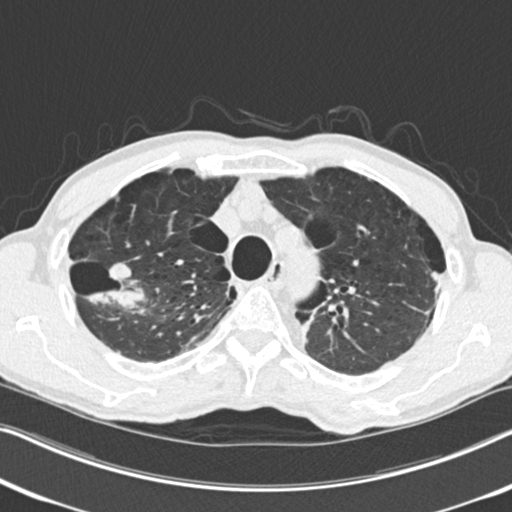
Low-dose screening chest CT, one axial slice; slice 195 of 251 in the series (ordered by position); reconstruction kernel B30f; 120 kVp; lung window (W 1500 / L -600 HU); 2 mm slice thickness; 512 × 512 image matrix, field of view 334 × 334 mm.
Outlined on this slice (expert manual segmentation):
- lesion 1 (tumor, upper lobe of right lung): box from (x=88, y=263) to (x=145, y=312) px